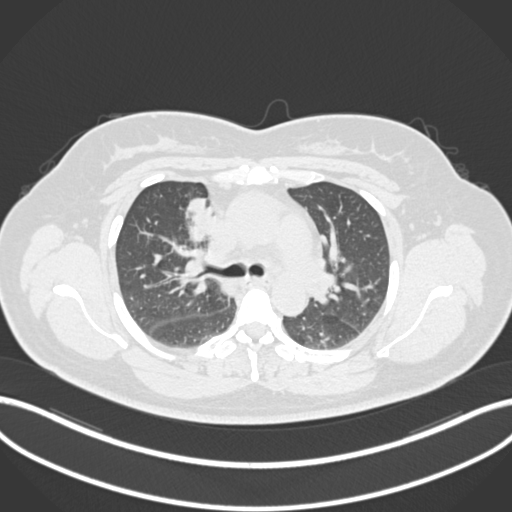
Chest CT, one axial slice; slice 118 of 183 in the series (ordered by position); lung window (W 1500 / L -600 HU); 1 mm slice thickness; 512 × 512 image matrix, field of view 400 × 400 mm. Patient: female, 46 years. Case-level facts recorded for this patient, not image findings: clinical TNM (as recorded): T2a N1 M0.
Structures marked on this image (rectangle marked by the reading radiologist):
- lung tumour (recorded histology: adenocarcinoma): box from (x=185, y=195) to (x=212, y=245) px